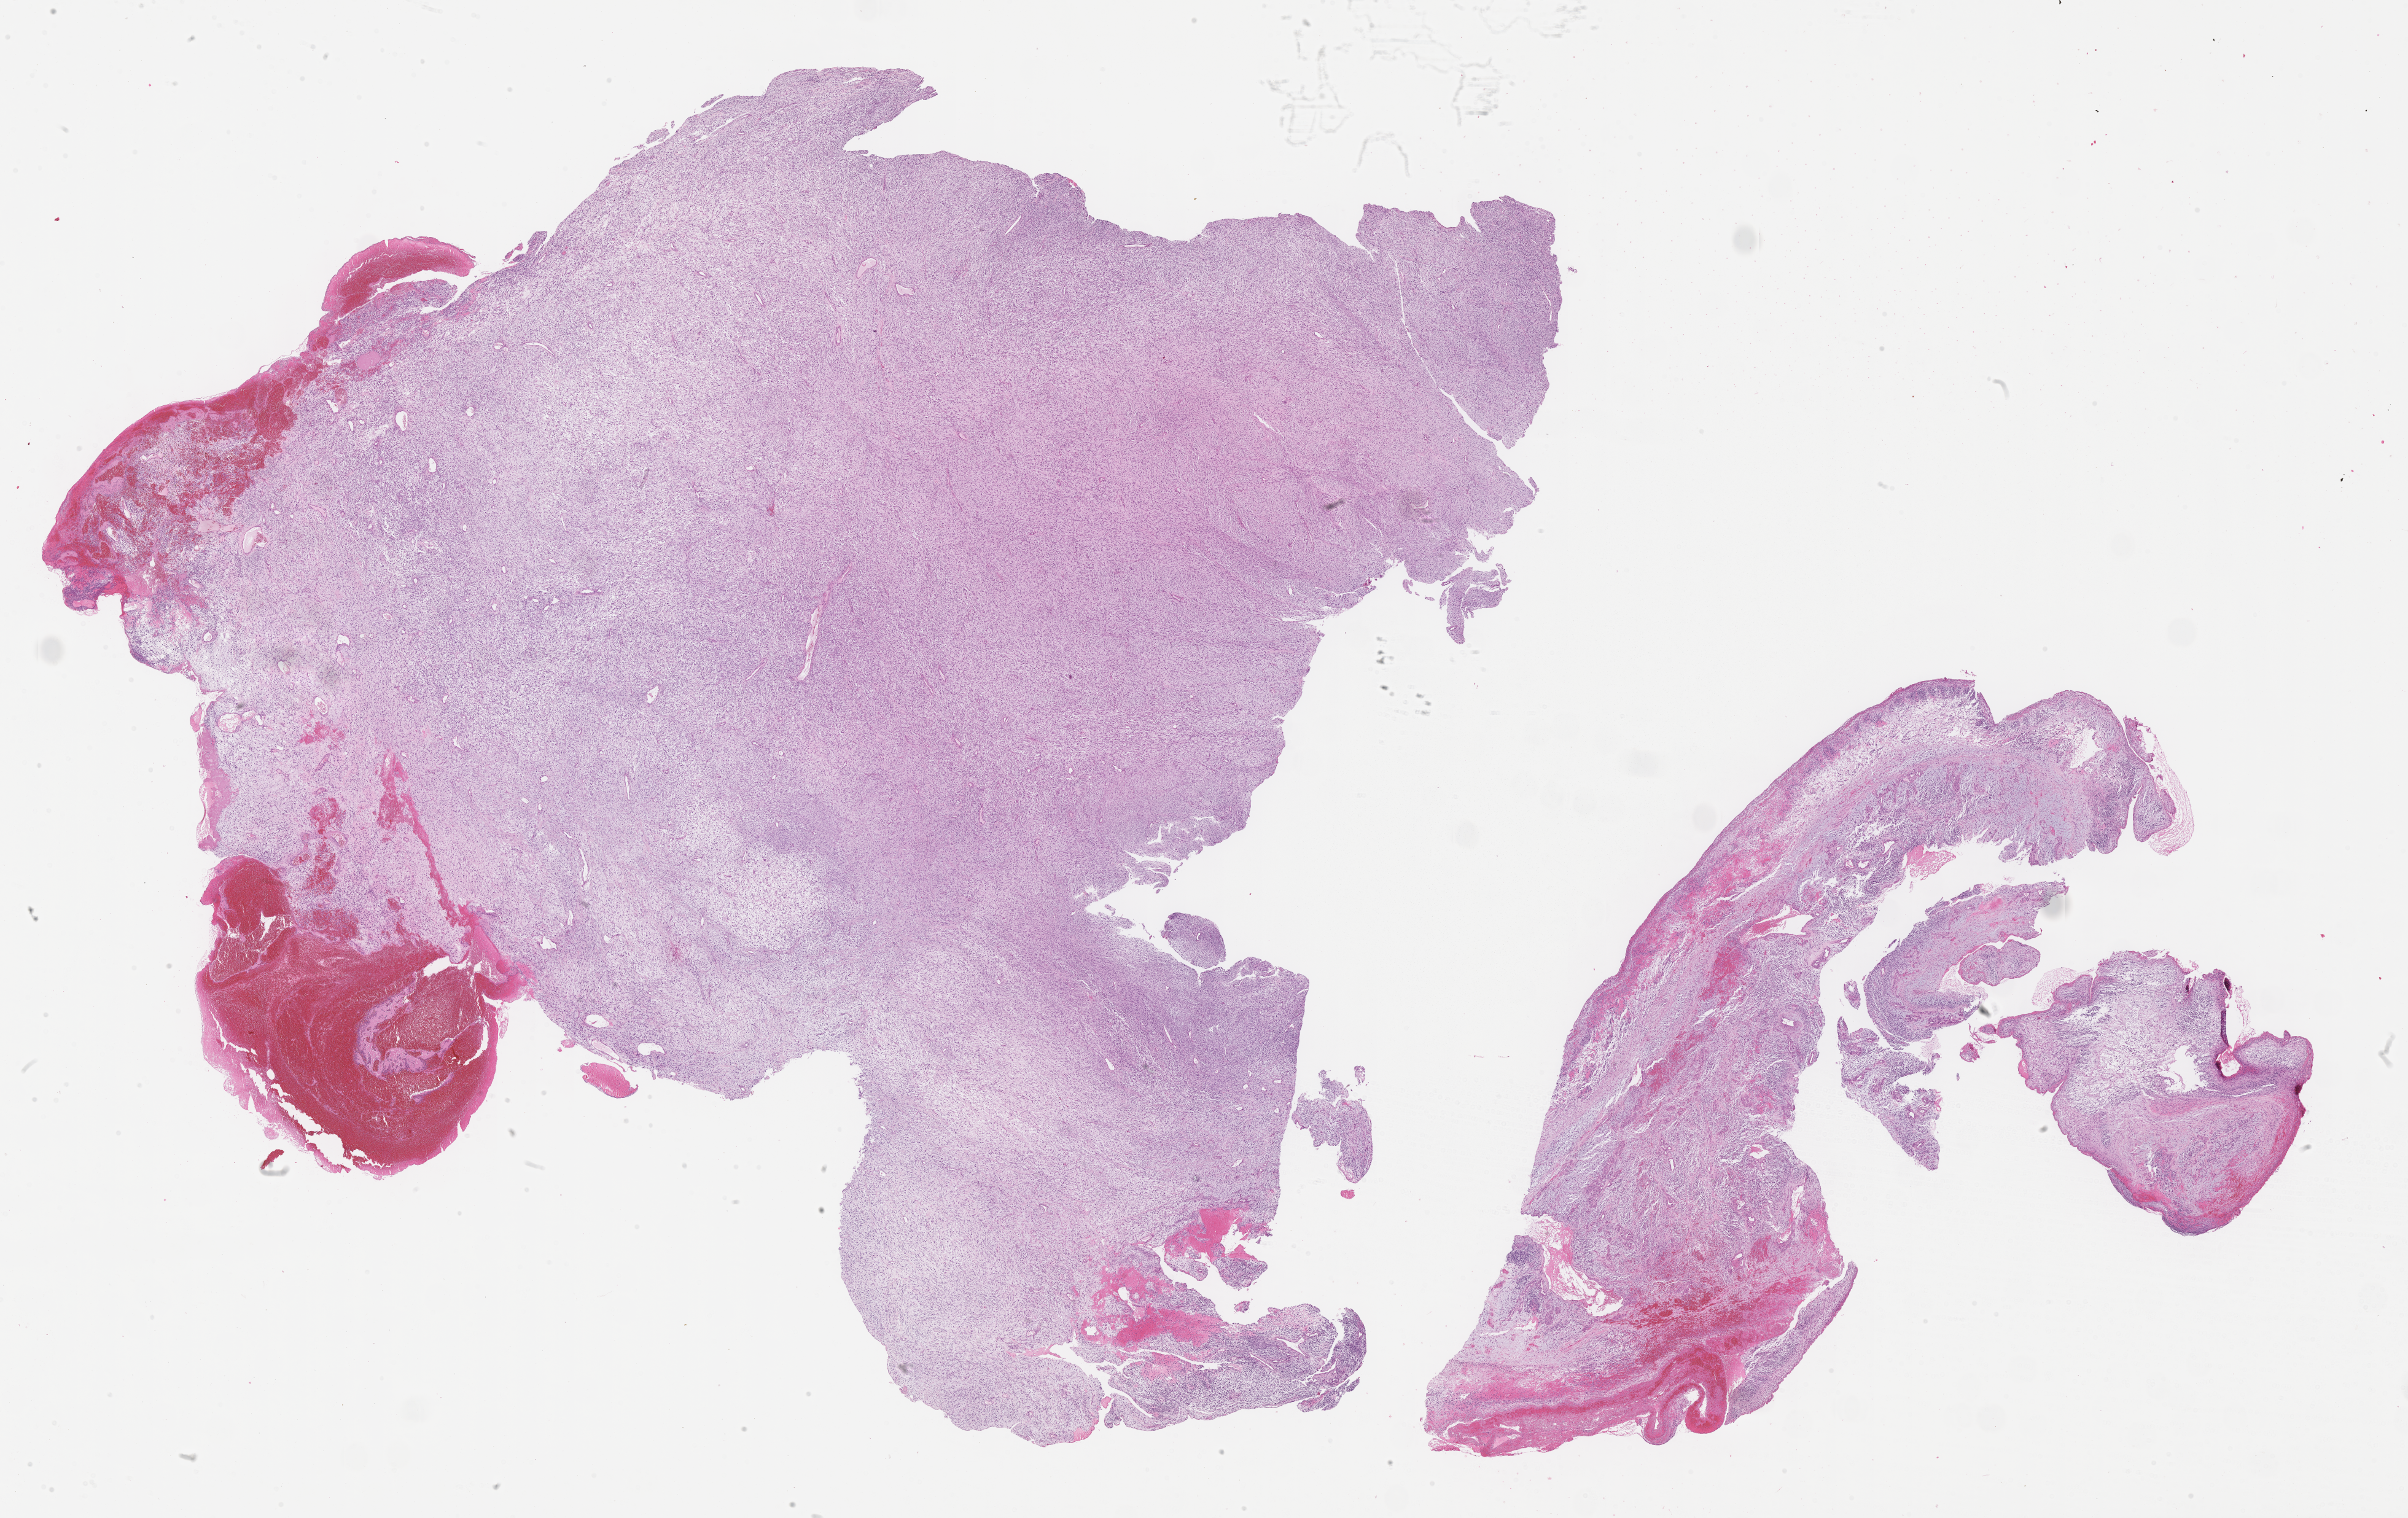
Whole-slide image, haematoxylin and eosin stain of tumor tissue — low-resolution overview of the scanned area, about 31.7 x 20.0 mm, FFPE section, sample anatomic site: soft tissue, abdomen. Female patient, age at diagnosis 2.1 years.
Stage (as recorded): 3. Diagnosis: rhabdomyosarcoma; histological classification: embryonal rhabdomyosarcoma. Metastatic status at presentation (as recorded): non-metastatic.